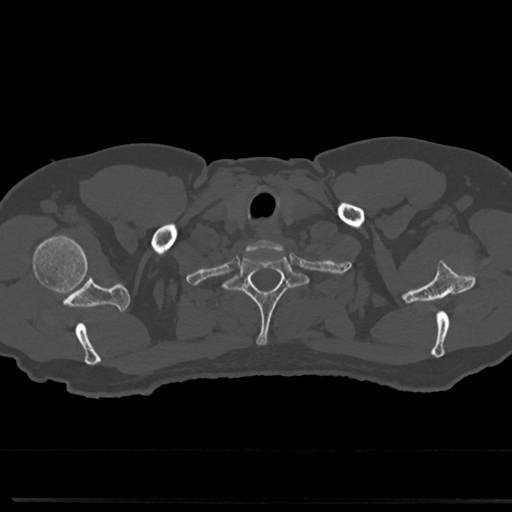
CT including the spine, one axial slice. Position 675 of 817 along the scan axis. Reconstruction kernel Br40s/3. Bone window (W 1800 / L 400 HU). 0.5 mm slice thickness. 512 × 512 image matrix. Male patient, age 61 years. Case-level facts recorded for this patient, not image findings: primary cancer: prostate.
Outlined on this slice (semi-automatically segmented with operator editing):
- T1 vertebra: bounding box (x1, y1, x2, y2) in pixels: (231, 251, 302, 347)
- T2 vertebra: (212, 292, 315, 313)